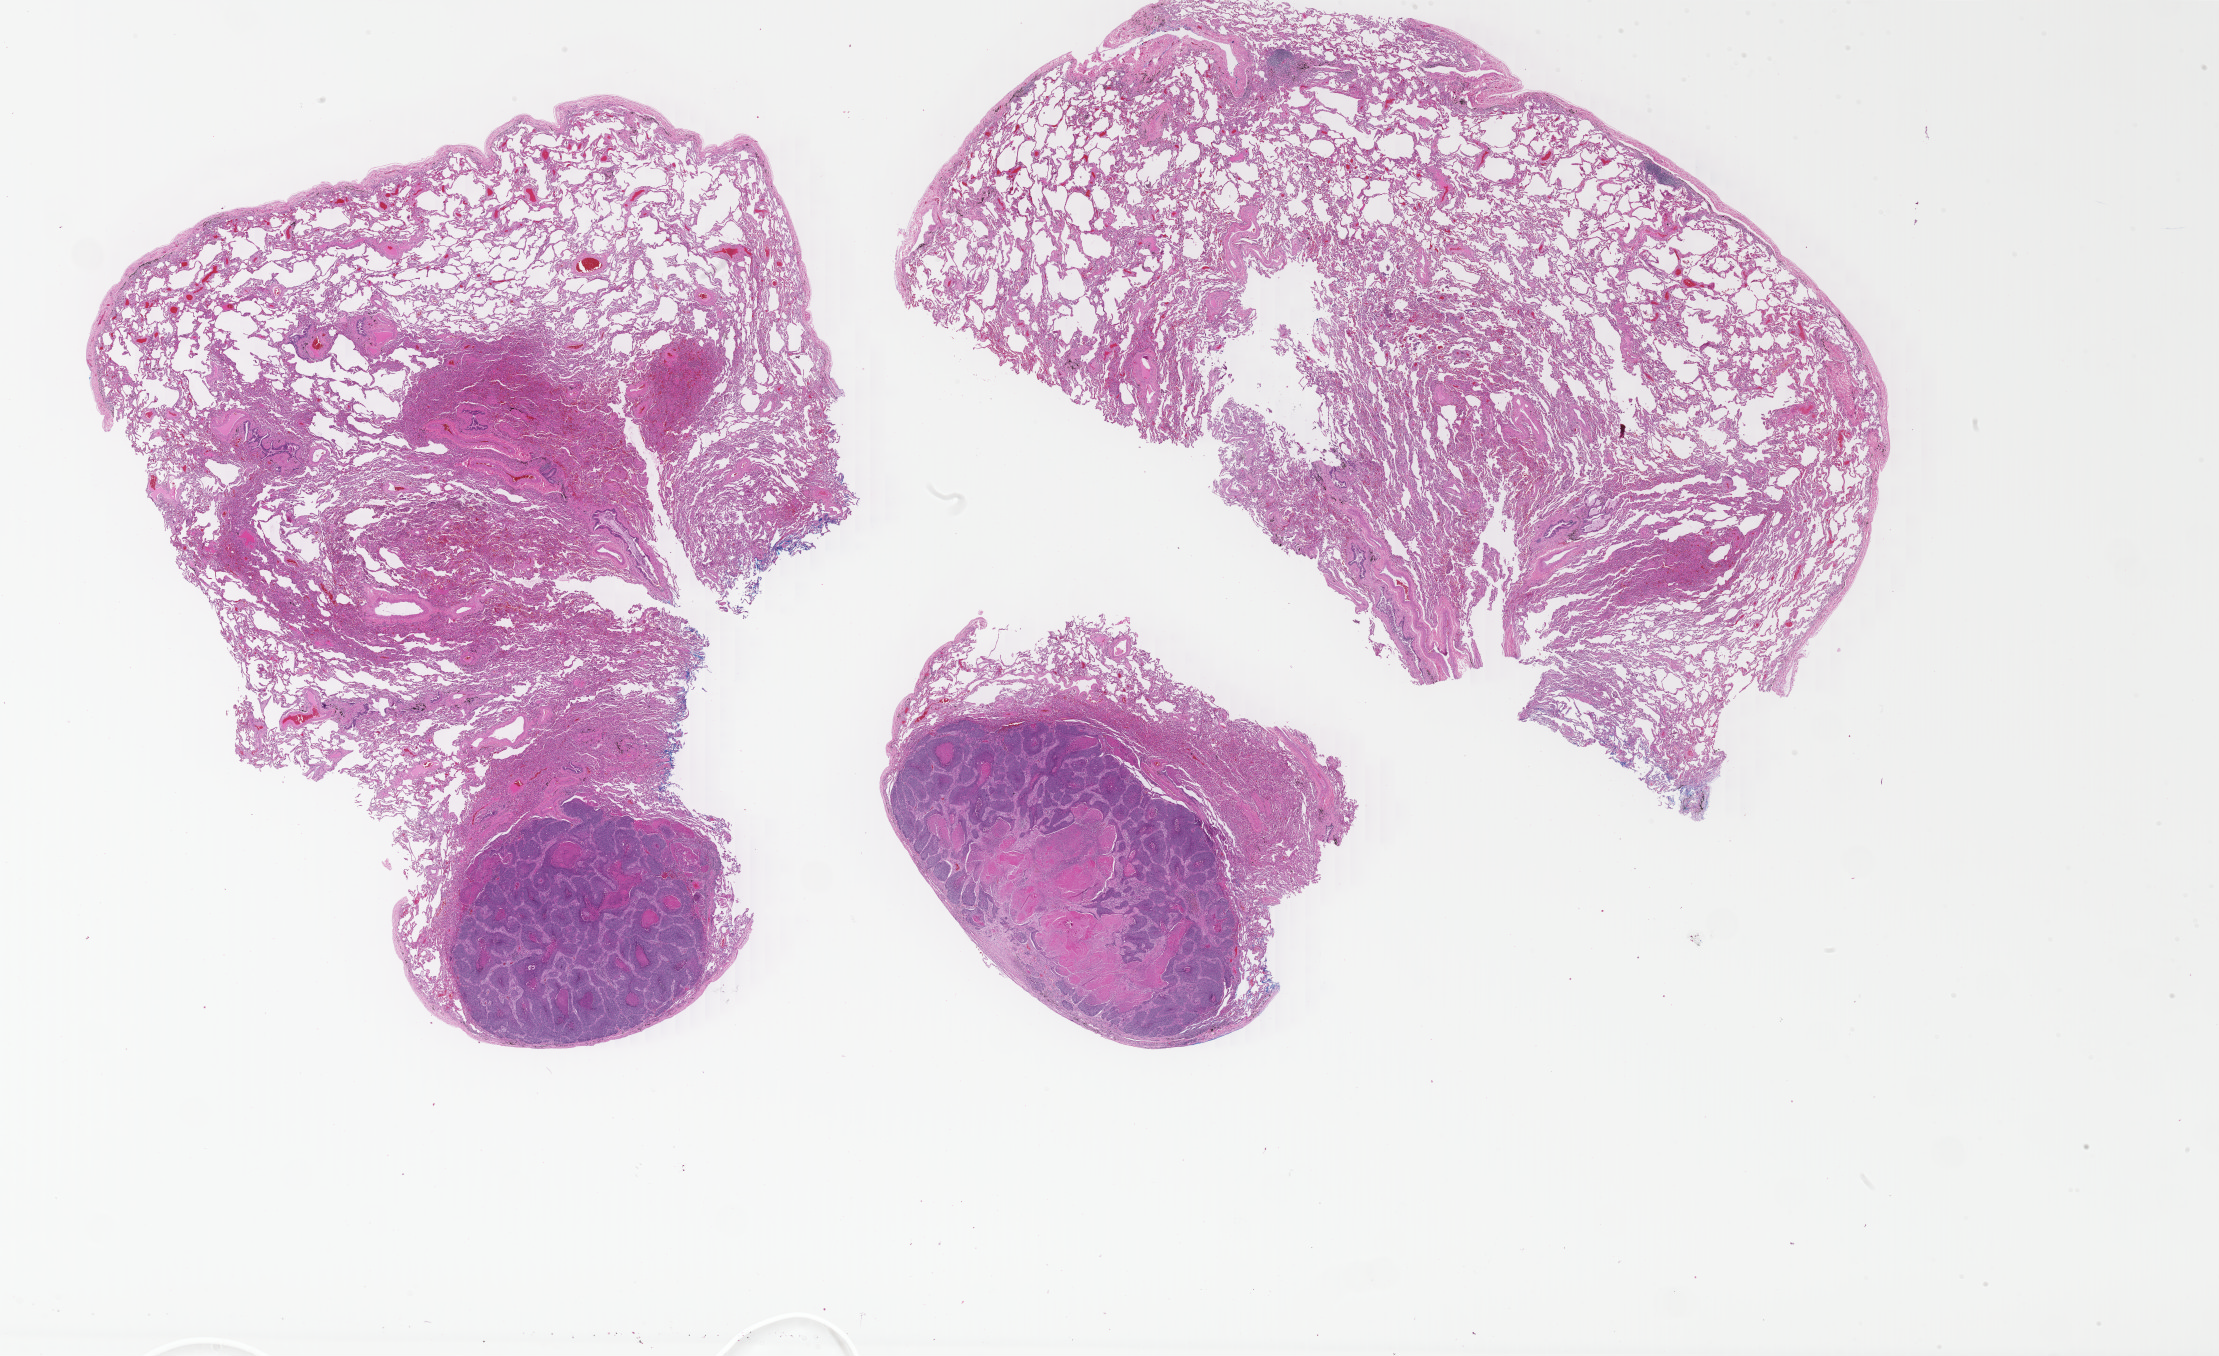
Whole-slide histology image, Hematoxylin and eosin (H&E) stained, low-resolution overview of the scanned area, about 35.7 x 21.8 mm. FFPE section. Sample: primary tumour, esophagus. Male, age 55 years at initial diagnosis. Histologic grade: GX (grade cannot be assessed).
* diagnosis: Squamous cell carcinoma, NOS (middle third of esophagus)